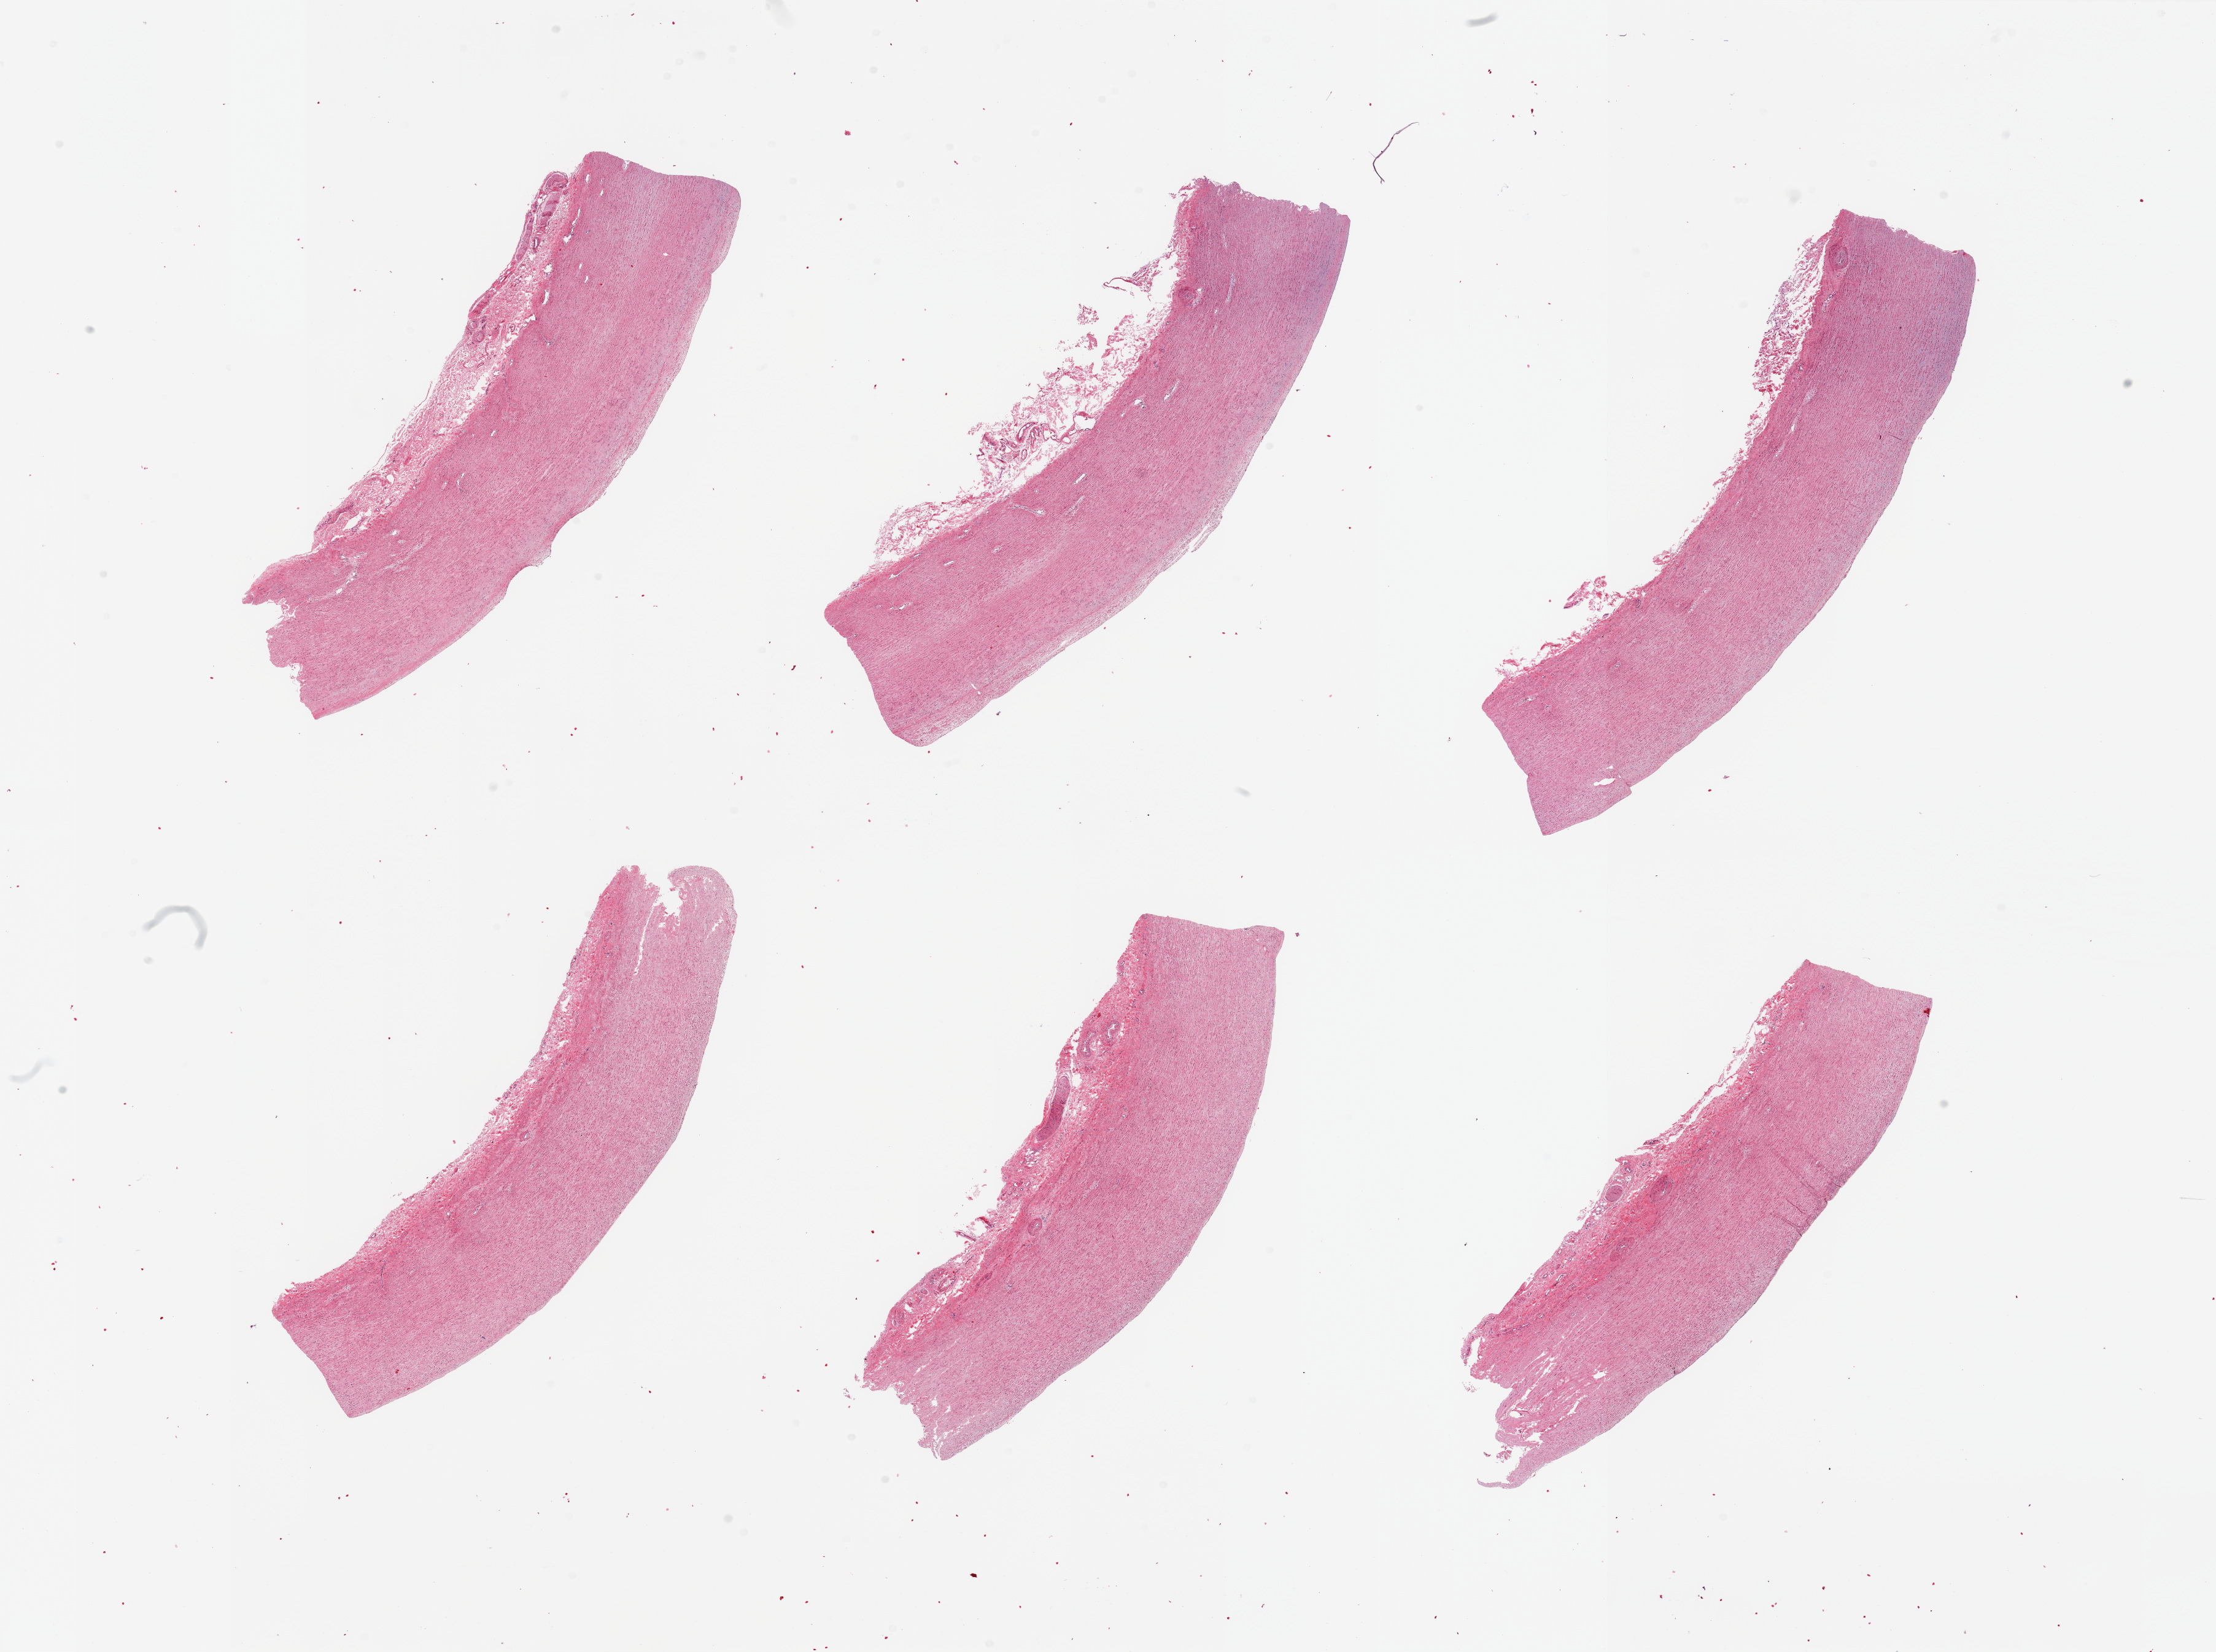
Digitized haematoxylin and eosin-stained section — whole scanned area (about 28.5 x 21.3 mm) shown as a low-resolution overview. PAXgene-fixed paraffin-embedded (PFPE) section. Section of aorta (target tissue). Donor tissue sample. Donor: male.
Pathologist's review note for this sample: 6 pieces; includes residual adventitia/nerve.